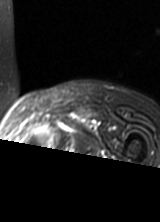
MRI of an extremity soft-tissue mass, one axial slice; T2-weighted fat-saturated; MR volume resampled by the dataset authors to the PET/CT grid (not the native acquisition matrix); 3.27 mm slice thickness; 160 × 222 image matrix, field of view 156 × 217 mm. Female patient. From the clinical record (not read from this slice): histological type: pleomorphic leiomyosarcoma; grade: high; site of the primary tumour: left thigh.
Outlined on this slice (expert contour drawn on MRI and transferred to this co-registered scan by the dataset authors):
- gross tumour volume including surrounding oedema: box from (x=29, y=127) to (x=64, y=151) px